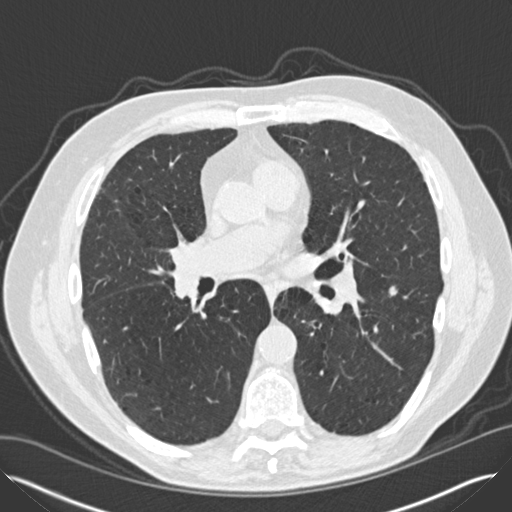
Low-dose screening chest CT, one axial slice; slice 74 of 149 in the series (ordered by position); reconstruction kernel B30f; lung window (W 1500 / L -600 HU); 2 mm slice thickness; 512 × 512 image matrix, field of view 370 × 370 mm.
Annotated regions visible in this slice (expert manual segmentation):
- lesion 1 (tumor, lower lobe of left lung): bounding box <389,286,405,298> (left, top, right, bottom; pixels)